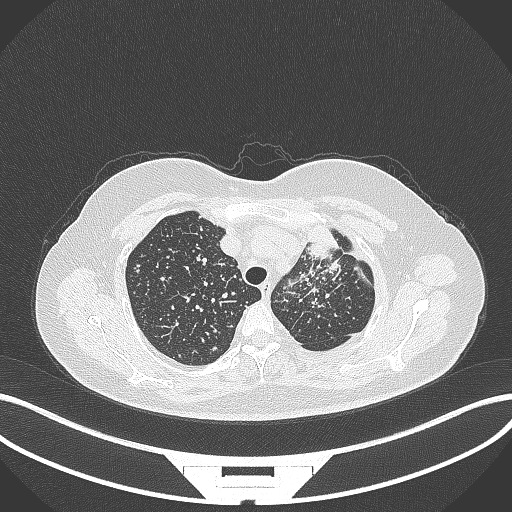
Chest CT, one axial slice. Reconstruction kernel B70f. 120 kVp. Lung window (W 1500 / L -600 HU). 1 mm slice thickness. 512 × 512 image matrix, field of view 400 × 400 mm. Patient: female, 49 years. Case-level facts recorded for this patient, not image findings: clinical TNM (as recorded): T1c N0 M1.
Annotated regions visible in this slice (bounding box drawn by a radiologist):
- lung tumour (recorded histology: adenocarcinoma): bounding box (x1, y1, x2, y2) in pixels: (305, 219, 341, 254)